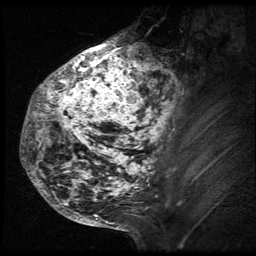
Breast MRI (dynamic contrast-enhanced), one sagittal slice. 3 images stored at this slice position (order not interpretable as contrast timing). 1.5 T. TE 4.2 ms, TR 9 ms. 2.5 mm slice thickness. 256 × 256 image matrix. Female patient, age 50 years. From the clinical record (not read from this slice): setting: breast cancer imaged before/during neoadjuvant chemotherapy; receptor status: triple-negative.
Structures marked on this image (semi-automatic segmentation, software-assisted and operator-edited):
- analysis volume of interest (the breast-tissue region the enhancement analysis was run in; not a lesion): box from (x=24, y=39) to (x=194, y=212) px
- tumour enhancement mask (voxels above the 140 % enhancement threshold inside the analysis volume of interest): (x=24, y=39)–(x=192, y=206)